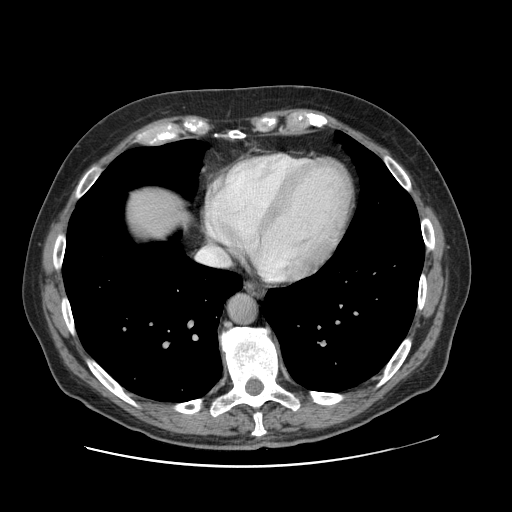
Contrast-enhanced abdominal CT, one axial slice. Slice 118 of 138 in the series (ordered by position). Intravenous contrast given. Soft-tissue window (W 400 / L 40 HU). 2.5 mm slice thickness. 512 × 512 image matrix, field of view 402 × 402 mm. Male patient, age 71 years. From the clinical record (not read from this slice): diagnosis: colorectal cancer liver metastases, imaged before liver resection; multiple liver metastases: no; largest metastasis: 3.3 cm.
Structures marked on this image (outlined manually by an expert reader):
- liver: box from (x=123, y=184) to (x=190, y=241) px
- planned liver remnant (the part of the liver to remain after resection): (x=123, y=184)–(x=188, y=242)